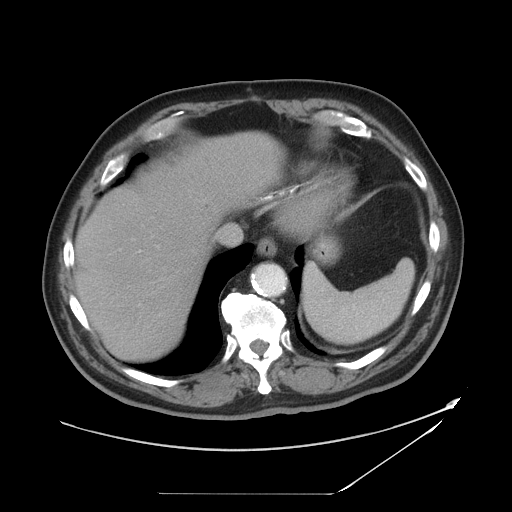
Contrast-enhanced abdominal CT, one axial slice; position 38 of 49 along the scan axis; reconstruction kernel STANDARD; 120 kVp; intravenous contrast given; soft-tissue window (W 400 / L 40 HU); 512 × 512 image matrix. Male patient, age 72 years. Case-level facts recorded for this patient, not image findings: diagnosis: colorectal cancer liver metastases, imaged before liver resection; multiple liver metastases: no; largest metastasis: 2.5 cm.
Annotated regions visible in this slice (outlined manually by an expert reader):
- liver: bounding box <78,135,277,358> (left, top, right, bottom; pixels)
- planned liver remnant (the part of the liver to remain after resection): <78,188,207,358>